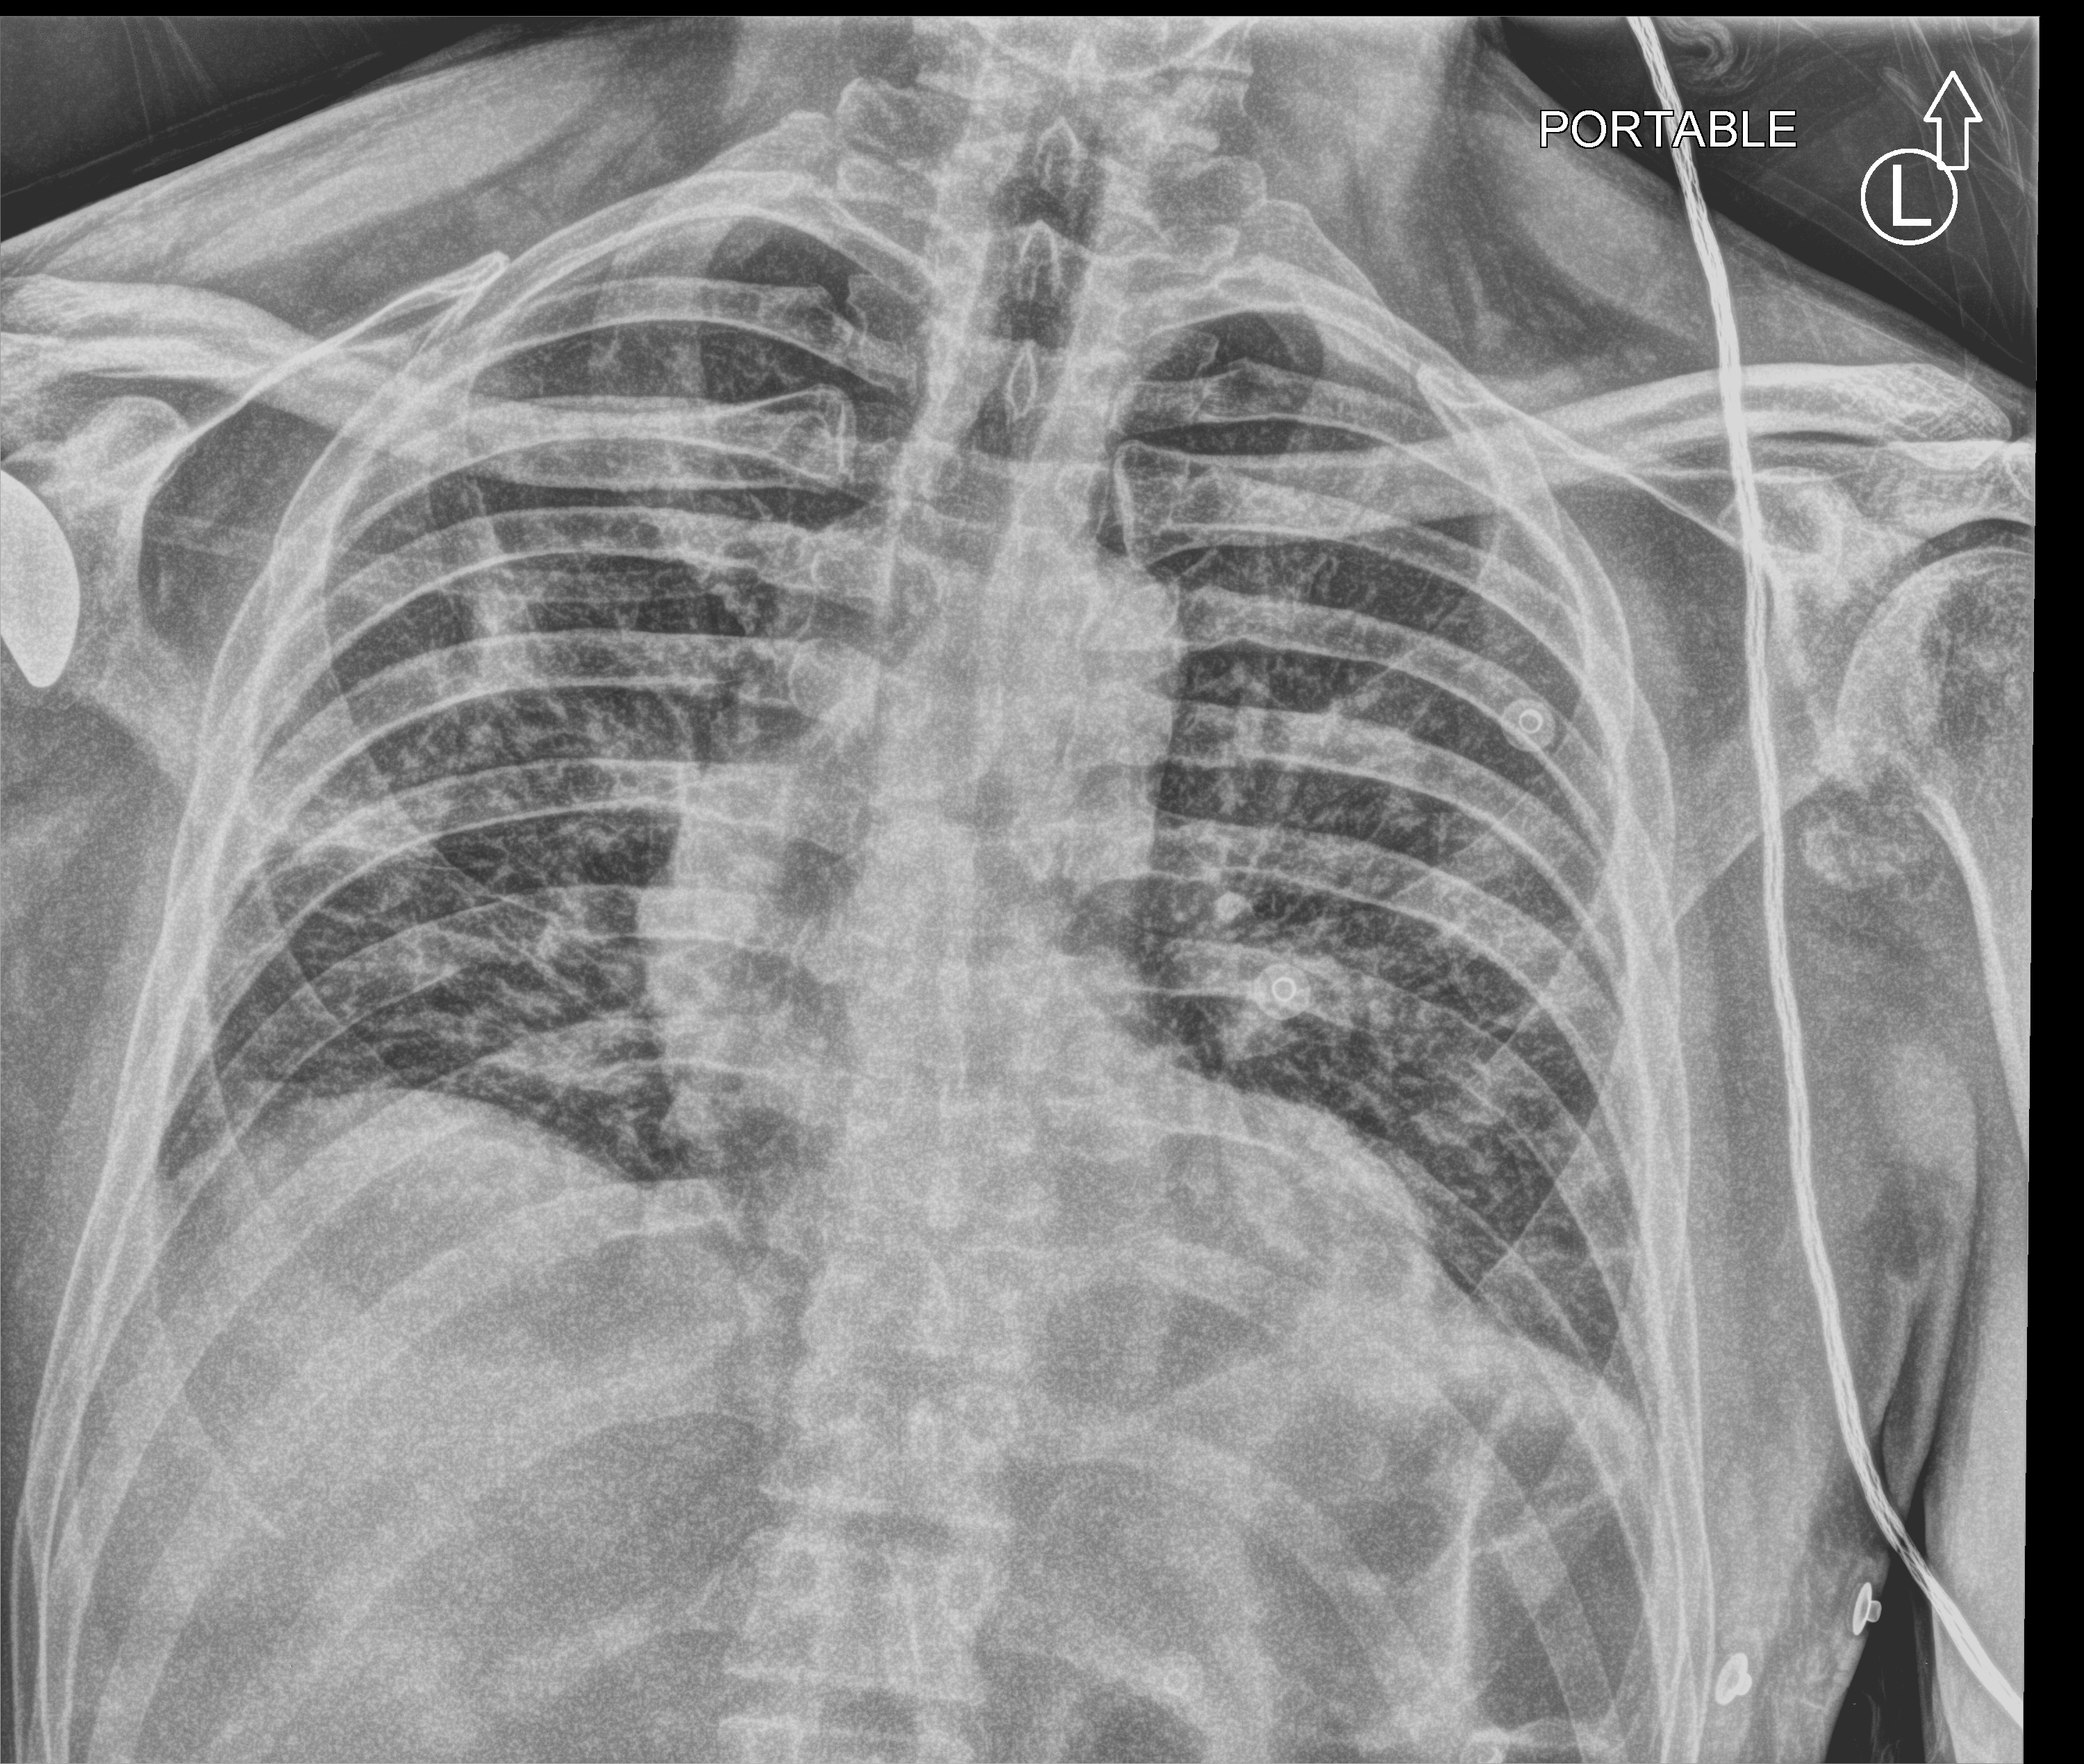
Bedside chest radiograph (computed radiography). Male patient hospitalised with COVID-19, age 60–74 years.
Hospital-stay facts (about this admission, not read from this image; timing relative to this image not recorded):
- admitted to intensive care during this hospital stay: no